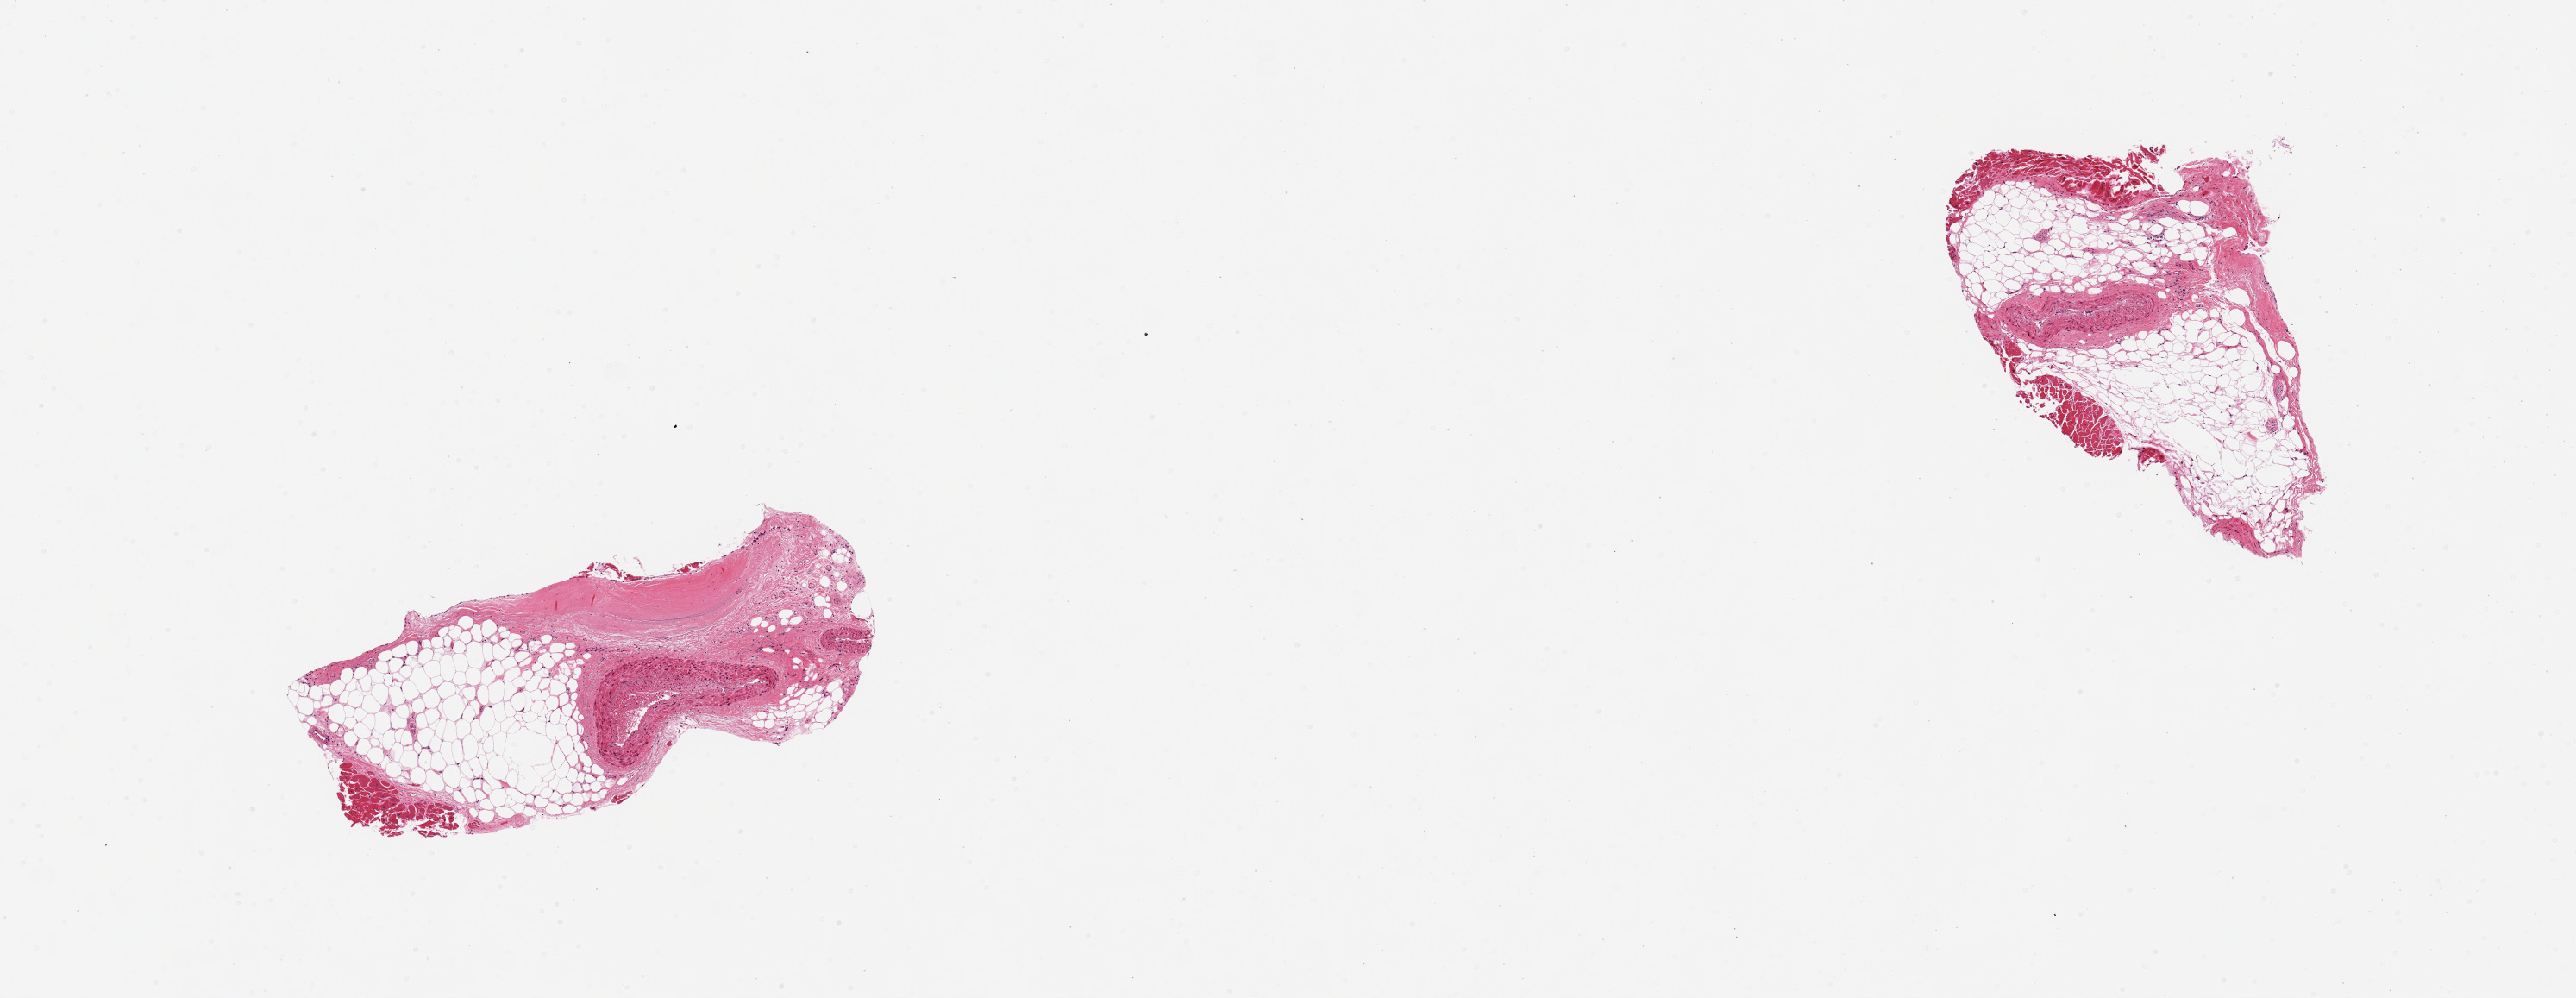
Whole-slide image, hematoxylin and eosin (H&E) stain, brightfield, whole scanned area (about 11.8 x 4.6 mm, slide scanned at 20x) shown as a low-resolution overview. PAXgene-fixed, paraffin-embedded tissue. Sampled site (target tissue): coronary artery. Donor tissue sample. Male donor.
Review note (as recorded): 2 pieces, artery represents ~10% of tissue with abundant attached fat and cardiac muscle.